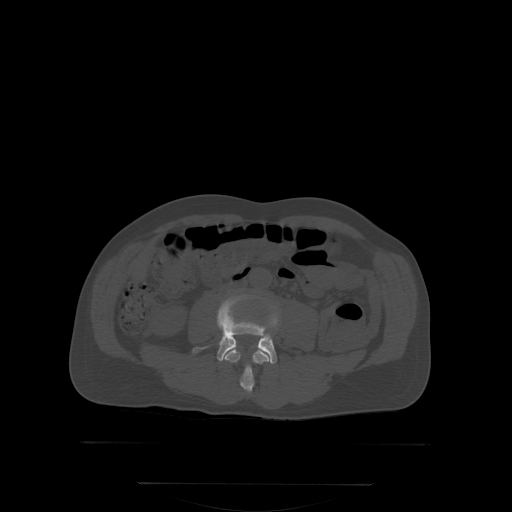
CT including the spine, one axial slice; position 114 of 350 along the scan axis; bone window (W 1800 / L 400 HU); 2.5 mm slice thickness; 512 × 512 image matrix. Patient: male, 58 years. Case-level facts recorded for this patient, not image findings: primary cancer: prostate; vertebrae with lytic lesions (as recorded): L1.
Structures marked on this image (semi-automatic segmentation, software-assisted and operator-edited):
- L3 vertebra: bounding box <226,349,269,392> (left, top, right, bottom; pixels)
- L4 vertebra: <192,298,279,362>